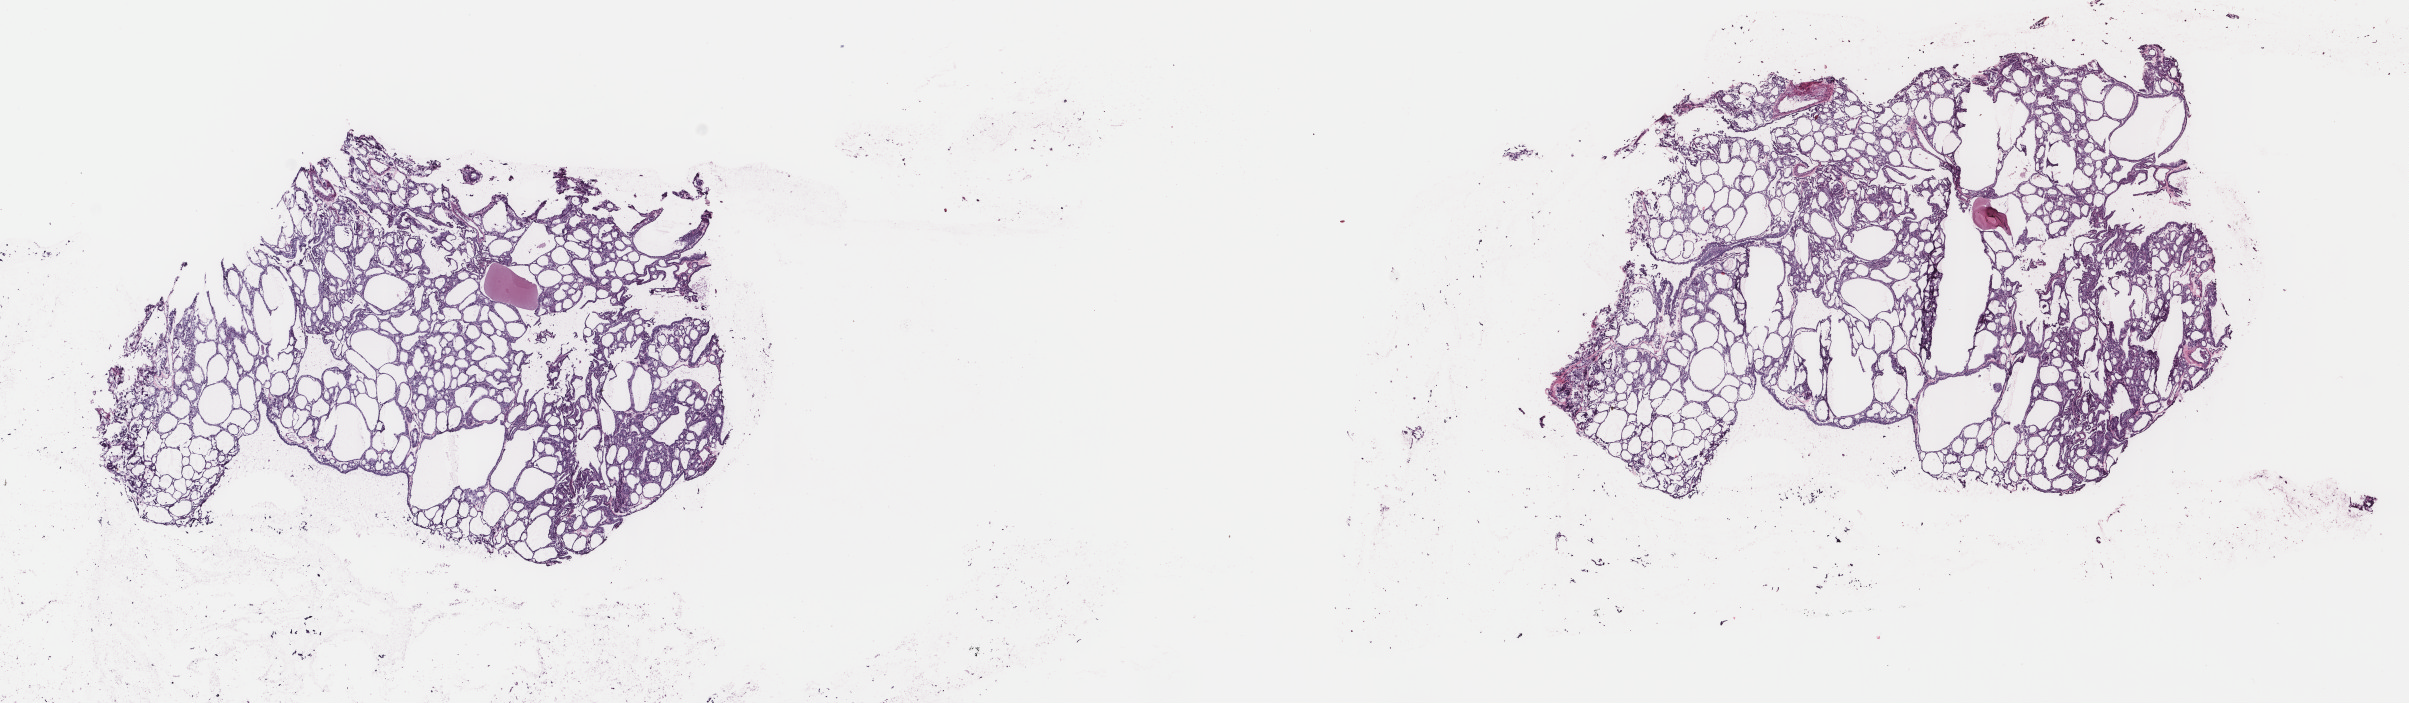
H&E-stained whole-slide image — a low-resolution overview of the entire scanned area, about 19.1 x 5.6 mm (slide scanned at 40x); frozen section; thyroid, primary tumour sample. Female patient; age at initial diagnosis 40 years. Composition of this section per pathologist review: tumour cells 90%, tumour nuclei 90%, normal cells 0%, stromal cells 10%, necrosis 0%. Inflammatory infiltration, as recorded: lymphocyte infiltration 0%, monocyte infiltration 0%, neutrophil infiltration 0%.
TNM: T1b N1a MX. Pathologic diagnosis: Papillary carcinoma, follicular variant (thyroid gland). AJCC pathologic stage: I (7th edition). Laterality: left. Lymph nodes positive (case pathology): 1 of 3 examined.